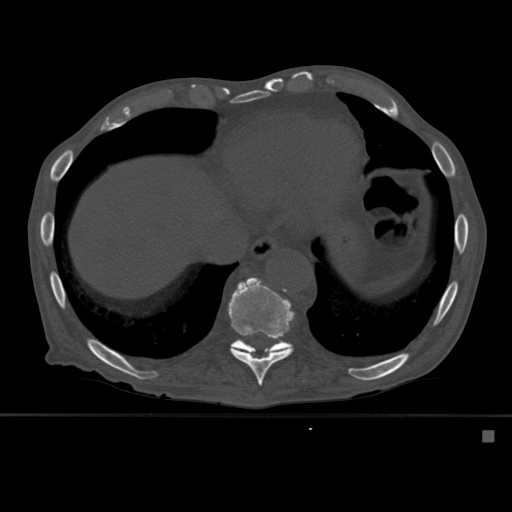
CT including the spine, one axial slice; slice 310 of 527 in the series (ordered by position); bone window (W 1800 / L 400 HU); 1.5 mm slice thickness; 512 × 512 image matrix. Patient: male, 78 years. From the clinical record (not read from this slice): primary cancer: prostate.
Structures marked on this image (semi-automatic segmentation, software-assisted and operator-edited):
- T10 vertebra: box from (x=228, y=277) to (x=295, y=386) px
- T11 vertebra: (x=234, y=339)–(x=294, y=355)